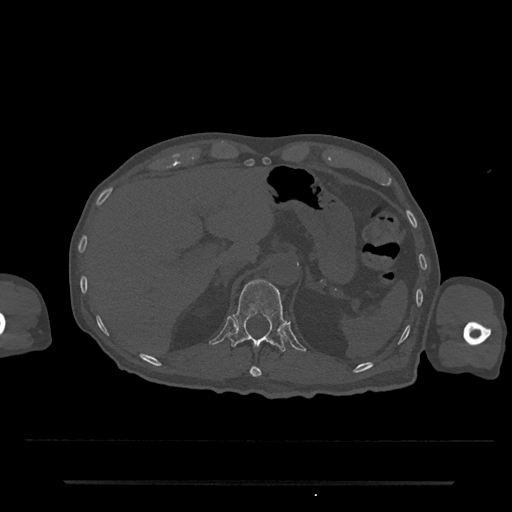
CT including the spine, one axial slice. Position 203 of 797 along the scan axis. Reconstruction kernel Br40s/3. Bone window (W 1800 / L 400 HU). 0.5 mm slice thickness. 512 × 512 image matrix. Patient: male, 74 years. From the clinical record (not read from this slice): primary cancer: prostate.
Annotated regions visible in this slice (semi-automatically segmented with operator editing):
- T11 vertebra: bounding box <250,366,262,378> (left, top, right, bottom; pixels)
- T12 vertebra: <228,279,287,352>